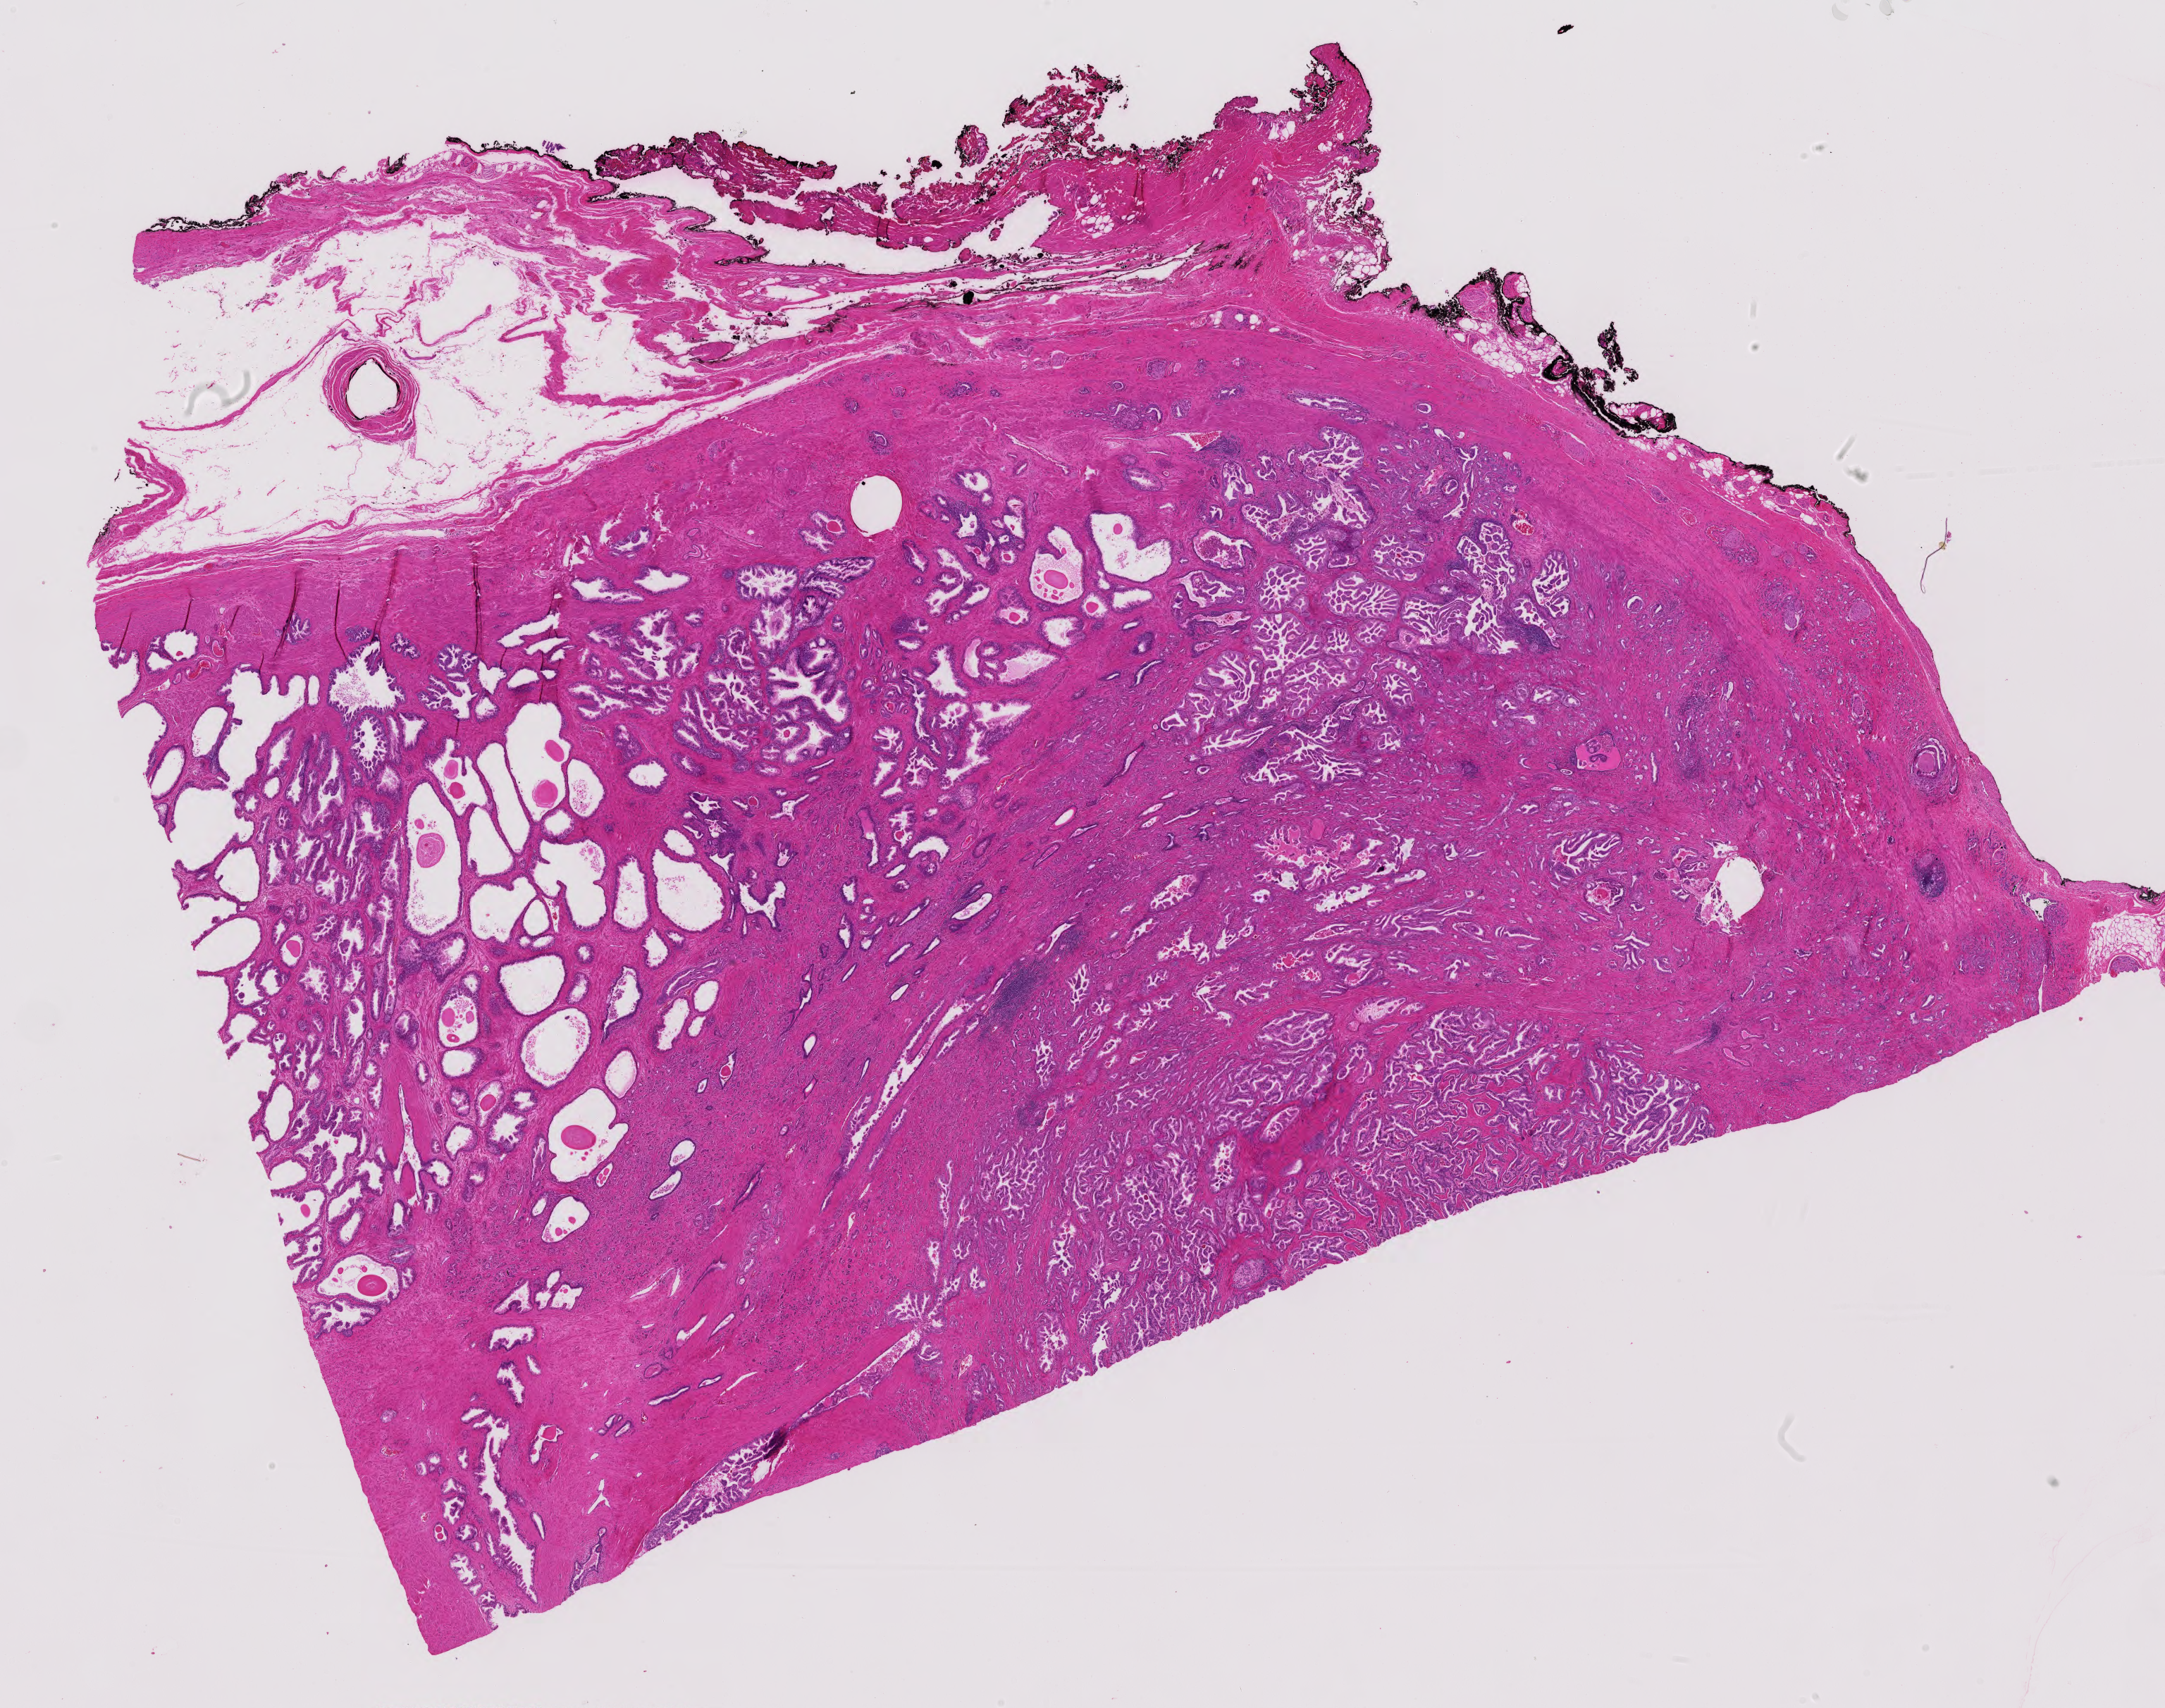
Digitized Hematoxylin and eosin (H&E) stained tissue section (whole slide), whole scanned area (about 22.3 x 17.6 mm, acquisition: 40x scan) shown as a low-resolution overview, FFPE section, primary tumour sample from the prostate. Male, age 69 years at initial diagnosis. Gleason score: 7 (4+3).
Lymph nodes positive (case pathology): 0 of 21 examined. Pathologic diagnosis: Adenocarcinoma, NOS (prostate gland). Laterality: bilateral.